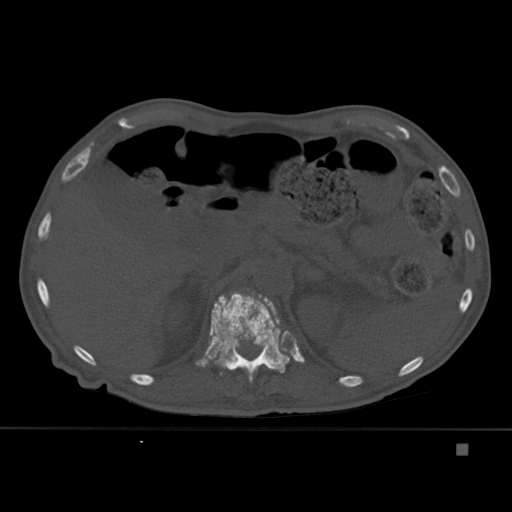
CT including the spine, one axial slice. Position 201 of 451 along the scan axis. Bone window (W 1800 / L 400 HU). 1.5 mm slice thickness. 512 × 512 image matrix, field of view 378 × 378 mm. Patient: male, 75 years. From the clinical record (not read from this slice): primary cancer: prostate.
Structures marked on this image (semi-automatically segmented with operator editing):
- T12 vertebra: bounding box [x1, y1, x2, y2] px = [208, 289, 290, 382]